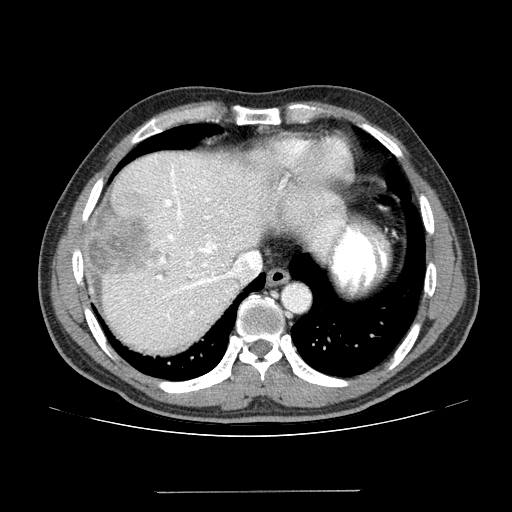
Contrast-enhanced abdominal CT (liver protocol), one axial slice; slice 112 of 131 in the series (ordered by position); 100 kVp; one of 2 acquisitions stored at this slice position; soft-tissue window (W 400 / L 40 HU); 2.5 mm slice thickness; 512 × 512 image matrix. From the clinical record (not read from this slice): diagnosis: hepatocellular carcinoma (patient treated with transarterial chemoembolisation; whether this scan precedes or follows treatment is not stated here); TNM stage (as recorded): Stage-I; Child-Pugh class: A; tumour nodularity: uninodular.
Annotated regions visible in this slice (semi-automatic segmentation, software-assisted and operator-edited):
- abdominal aorta: bounding box (x1, y1, x2, y2) in pixels: (282, 284, 309, 312)
- liver parenchyma outside the tumour (the mass and vessels are separate outlines, so this box may not span the whole liver): (80, 151, 307, 354)
- mass: (86, 212, 160, 285)
- liver vessels: (115, 157, 283, 322)